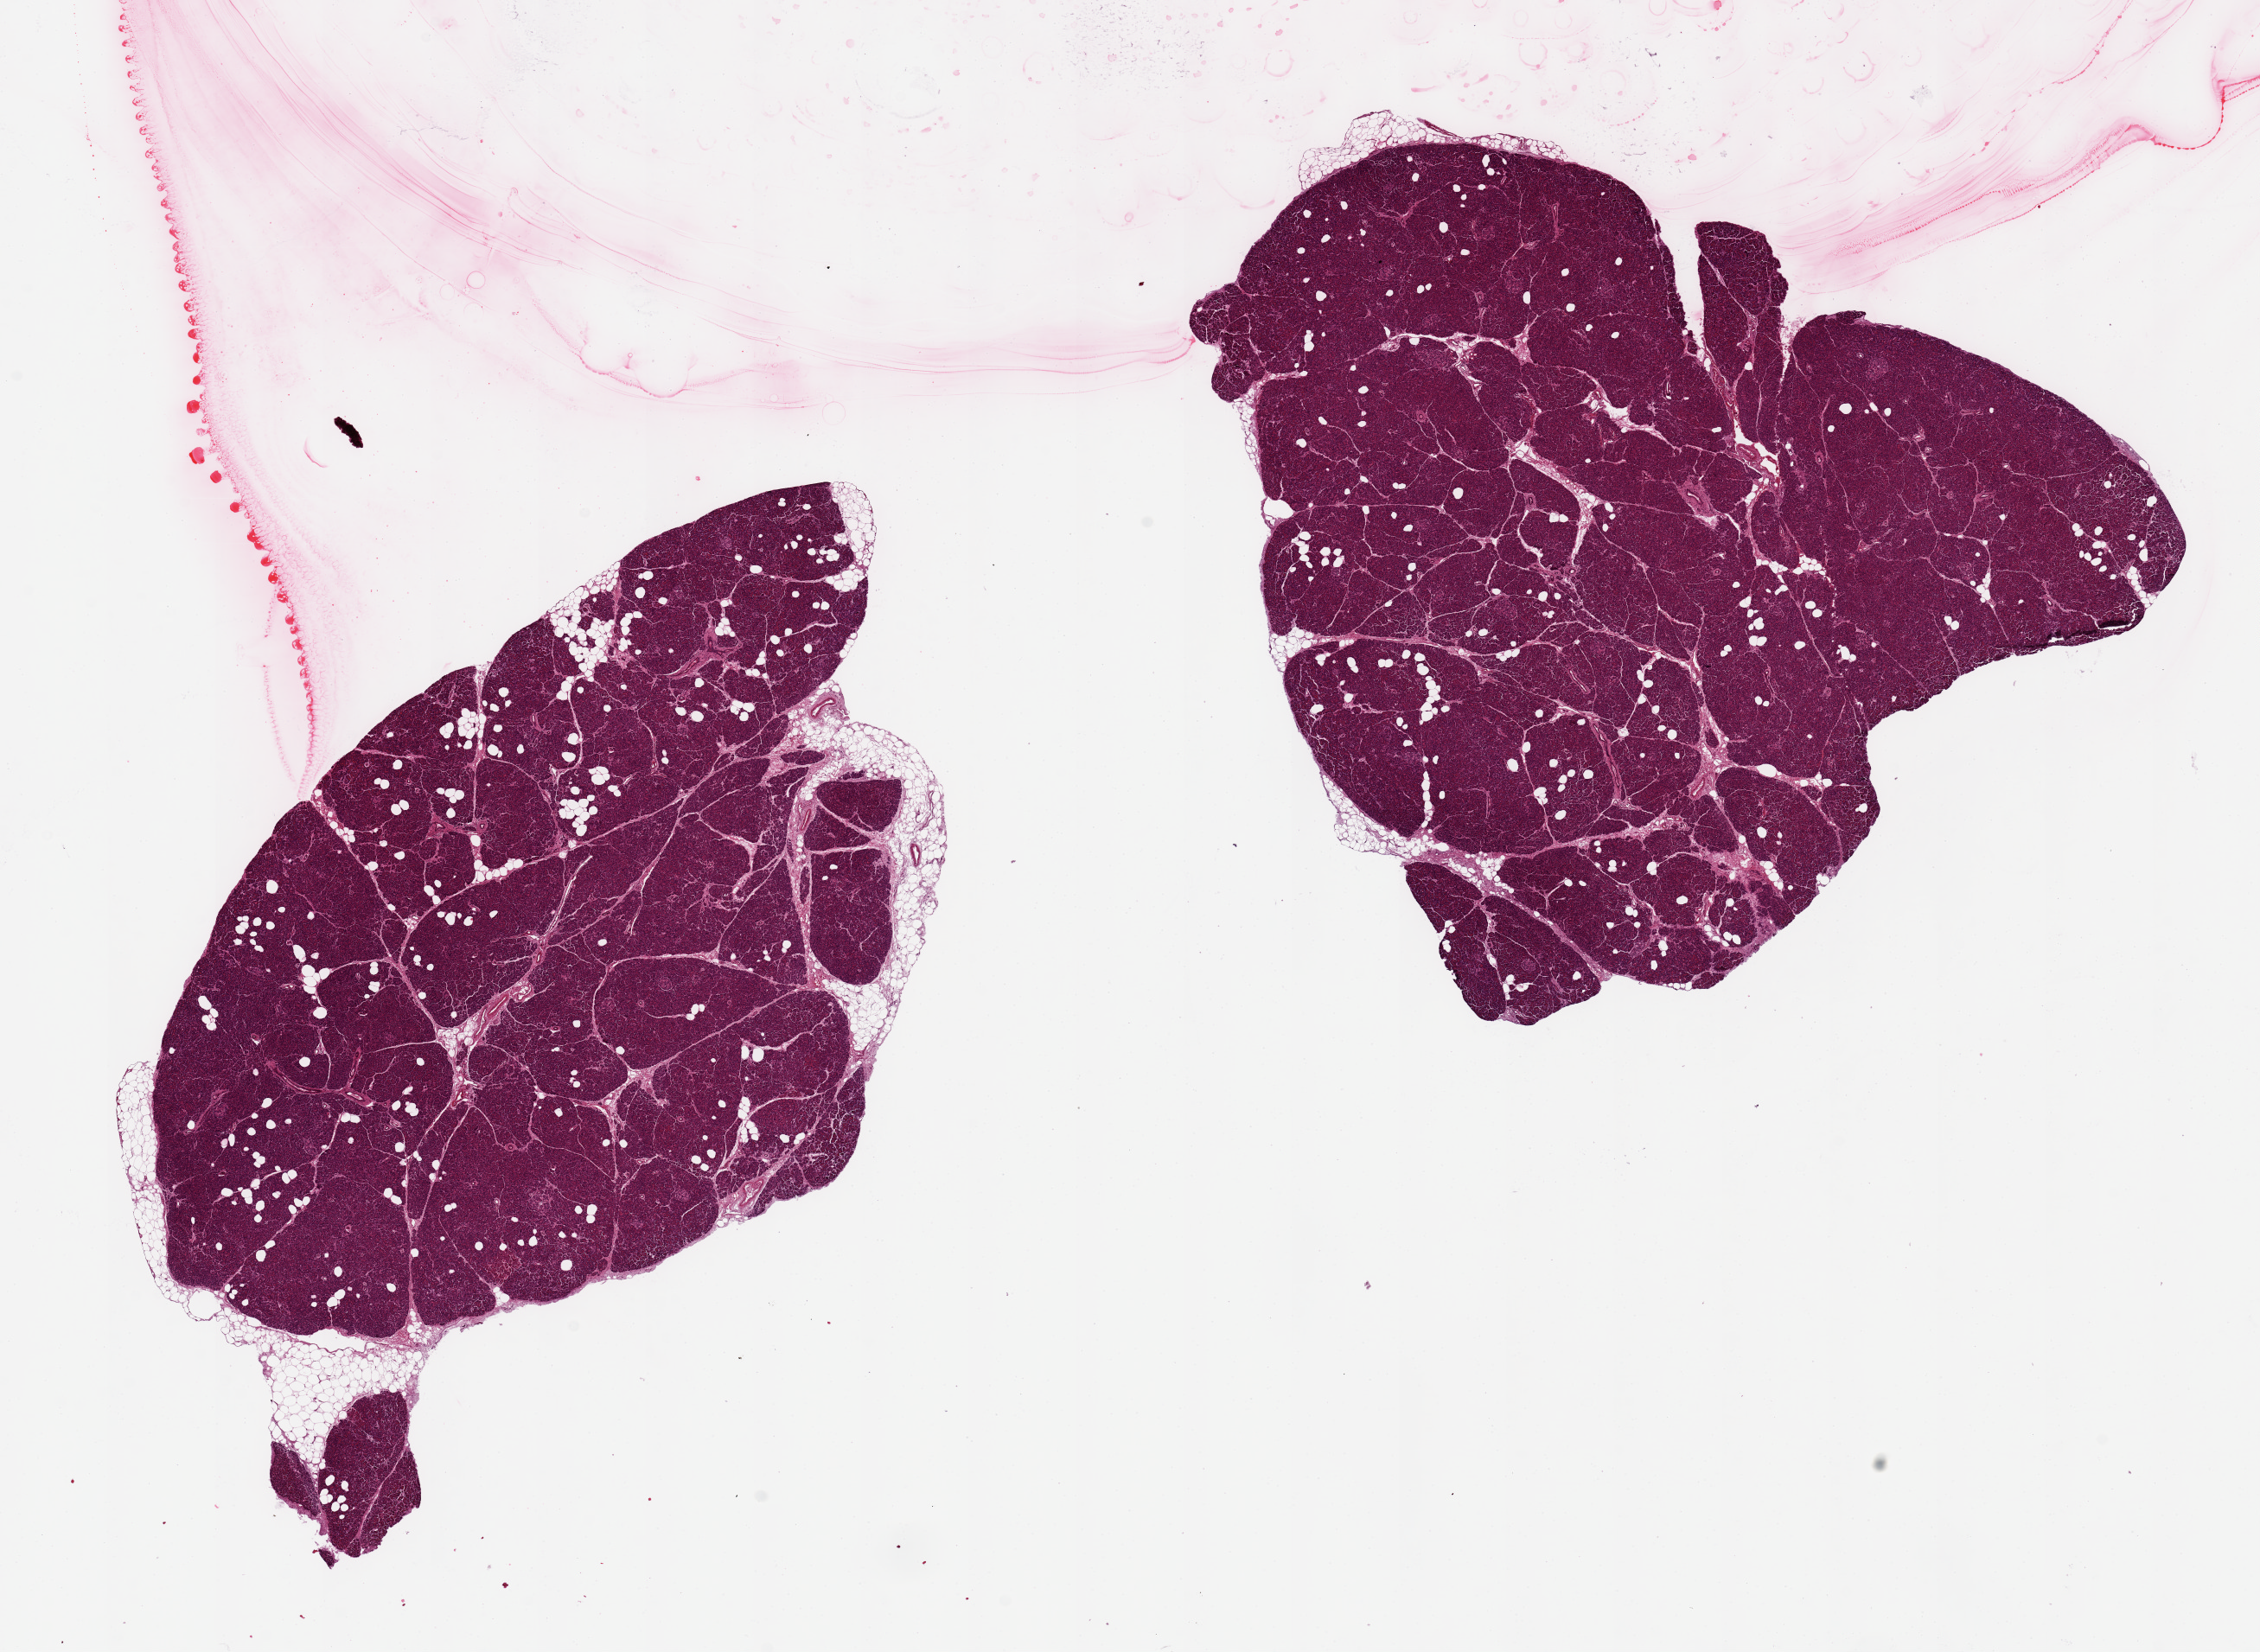
Digitized haematoxylin and eosin-stained section — shown as a low-resolution overview of the whole scanned area (about 20.7 x 15.1 mm, from a 20x scan), PAXgene-fixed, paraffin-embedded tissue, sampled site (target tissue): pancreas, tissue donor sample. Male donor.
Reviewer comment on this tissue sample: 2 pieces ~8x7mm; Islets well visualized; Minimal fat/saponification; well preserved specimen.